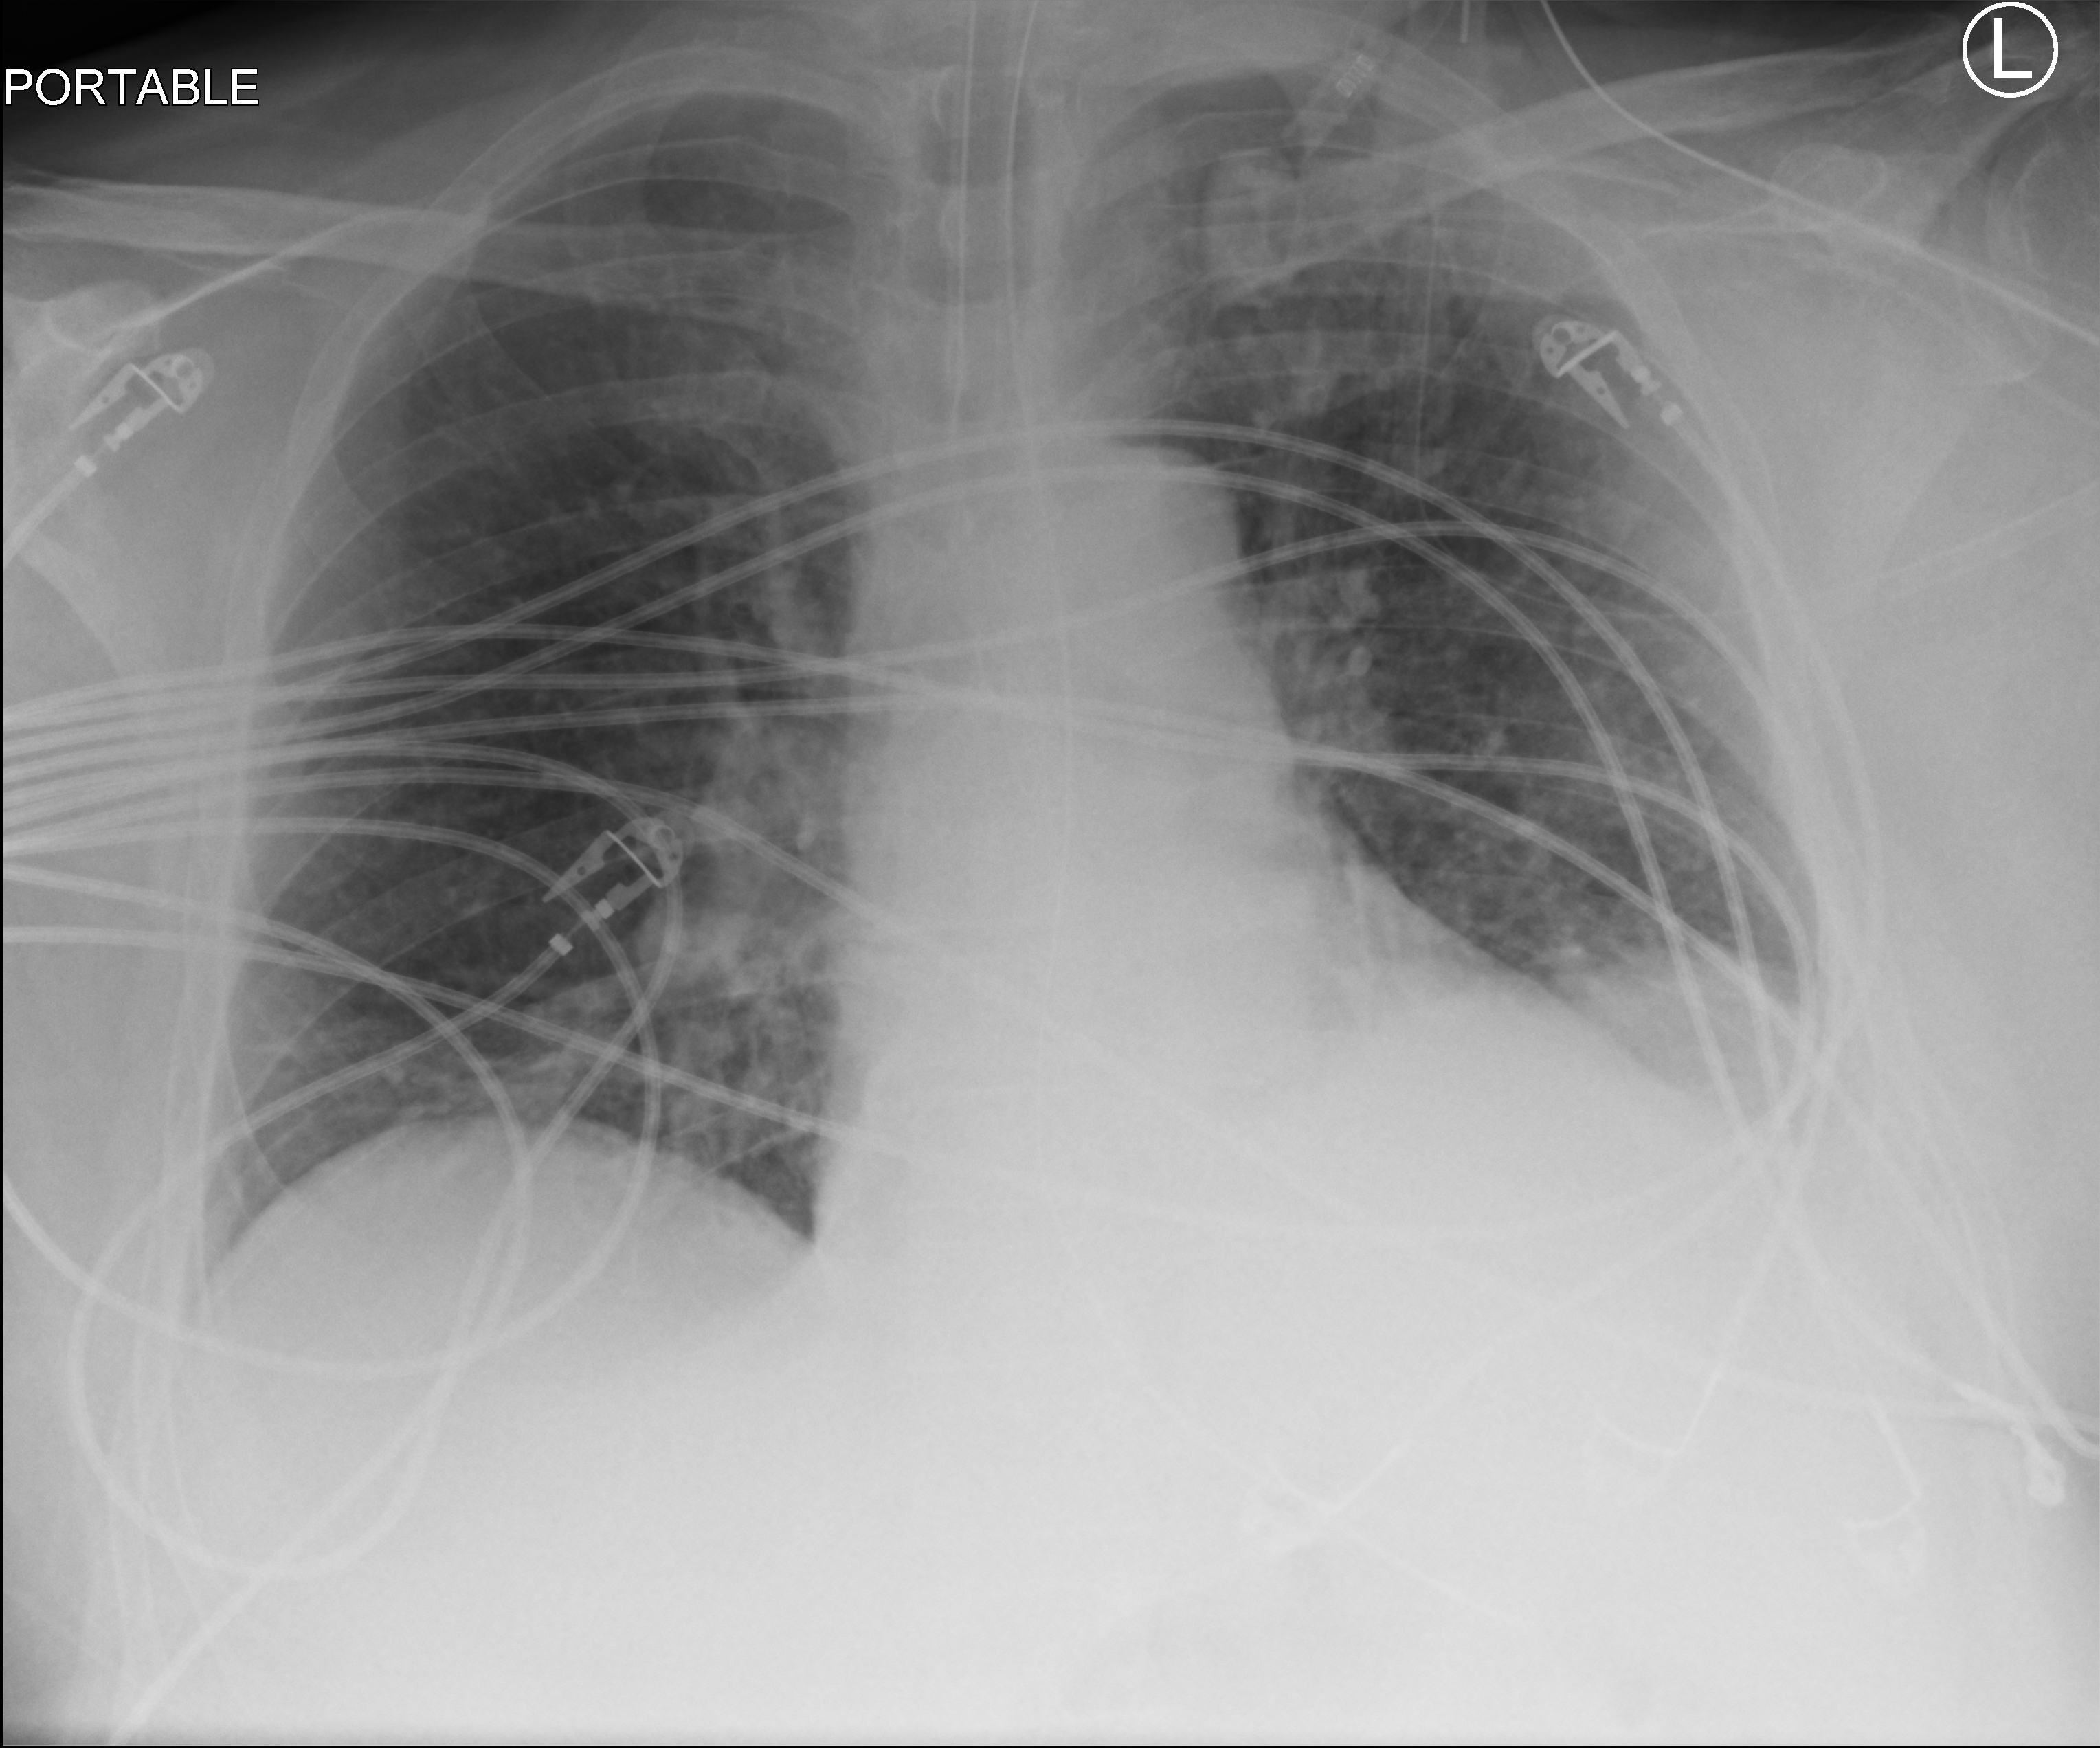
Chest X-ray (portable), anteroposterior (AP) projection. Patient hospitalised with COVID-19; male, aged 60–74 years.
Admission-level facts for this patient (not findings on this image; timing relative to this image not recorded): hypertension (admission record): no.